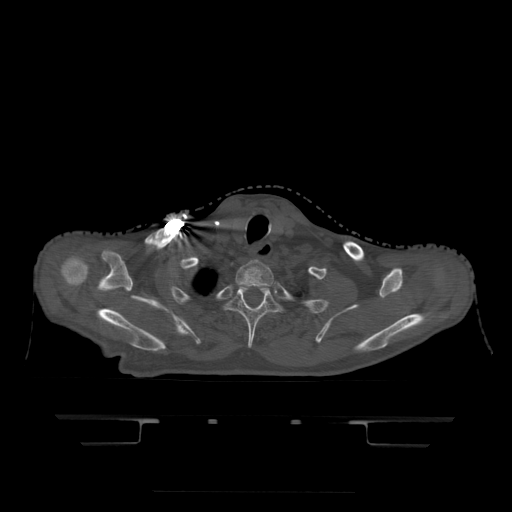
CT including the spine, one axial slice; slice 389 of 522 in the series (ordered by position); bone window (W 1800 / L 400 HU); 1.25 mm slice thickness; 512 × 512 image matrix. Patient age 68 years. From the clinical record (not read from this slice): primary cancer: urothelial.
Annotated regions visible in this slice (semi-automatic segmentation, software-assisted and operator-edited):
- T1 vertebra: bounding box (x1, y1, x2, y2) in pixels: (235, 260, 274, 288)
- T2 vertebra: (227, 286, 281, 349)